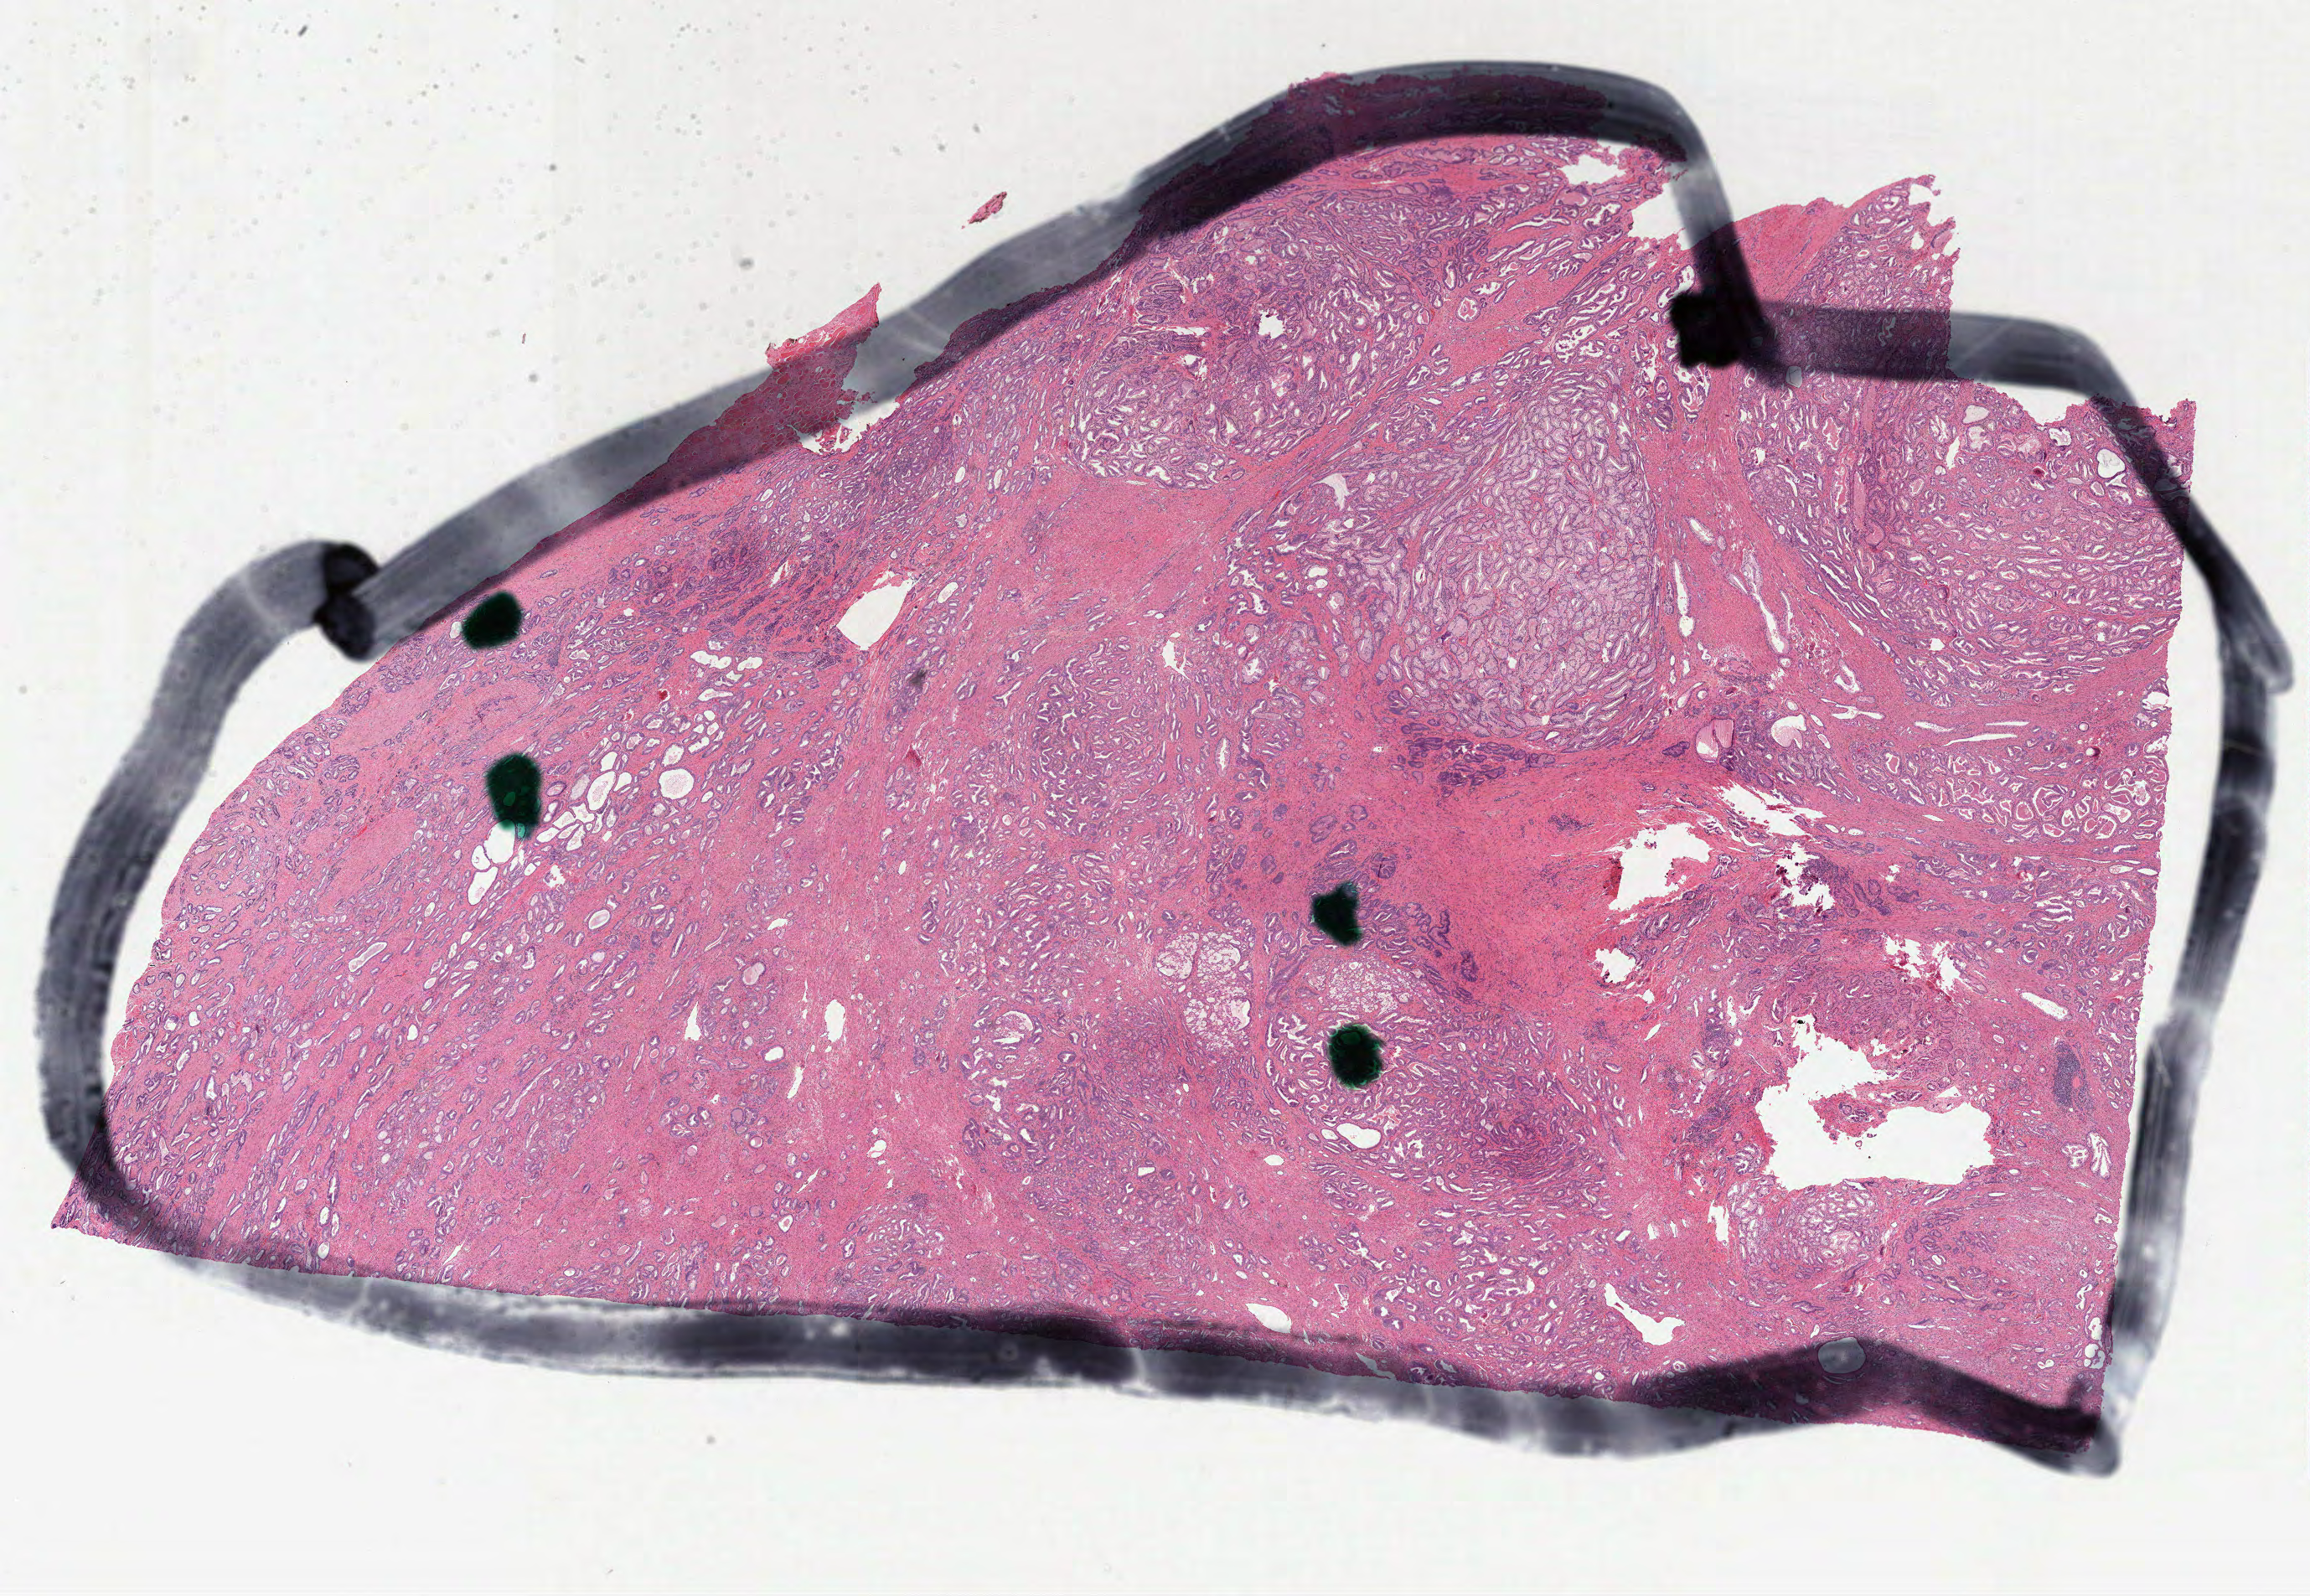
H&E whole-slide image — shown as a low-resolution overview of the whole scanned area (about 22.2 x 15.4 mm, from a 40x scan); formalin-fixed paraffin-embedded (FFPE) diagnostic section; prostate, primary tumour sample. Male patient; age at initial diagnosis 61 years.
Histologic diagnosis: Acinar cell carcinoma.